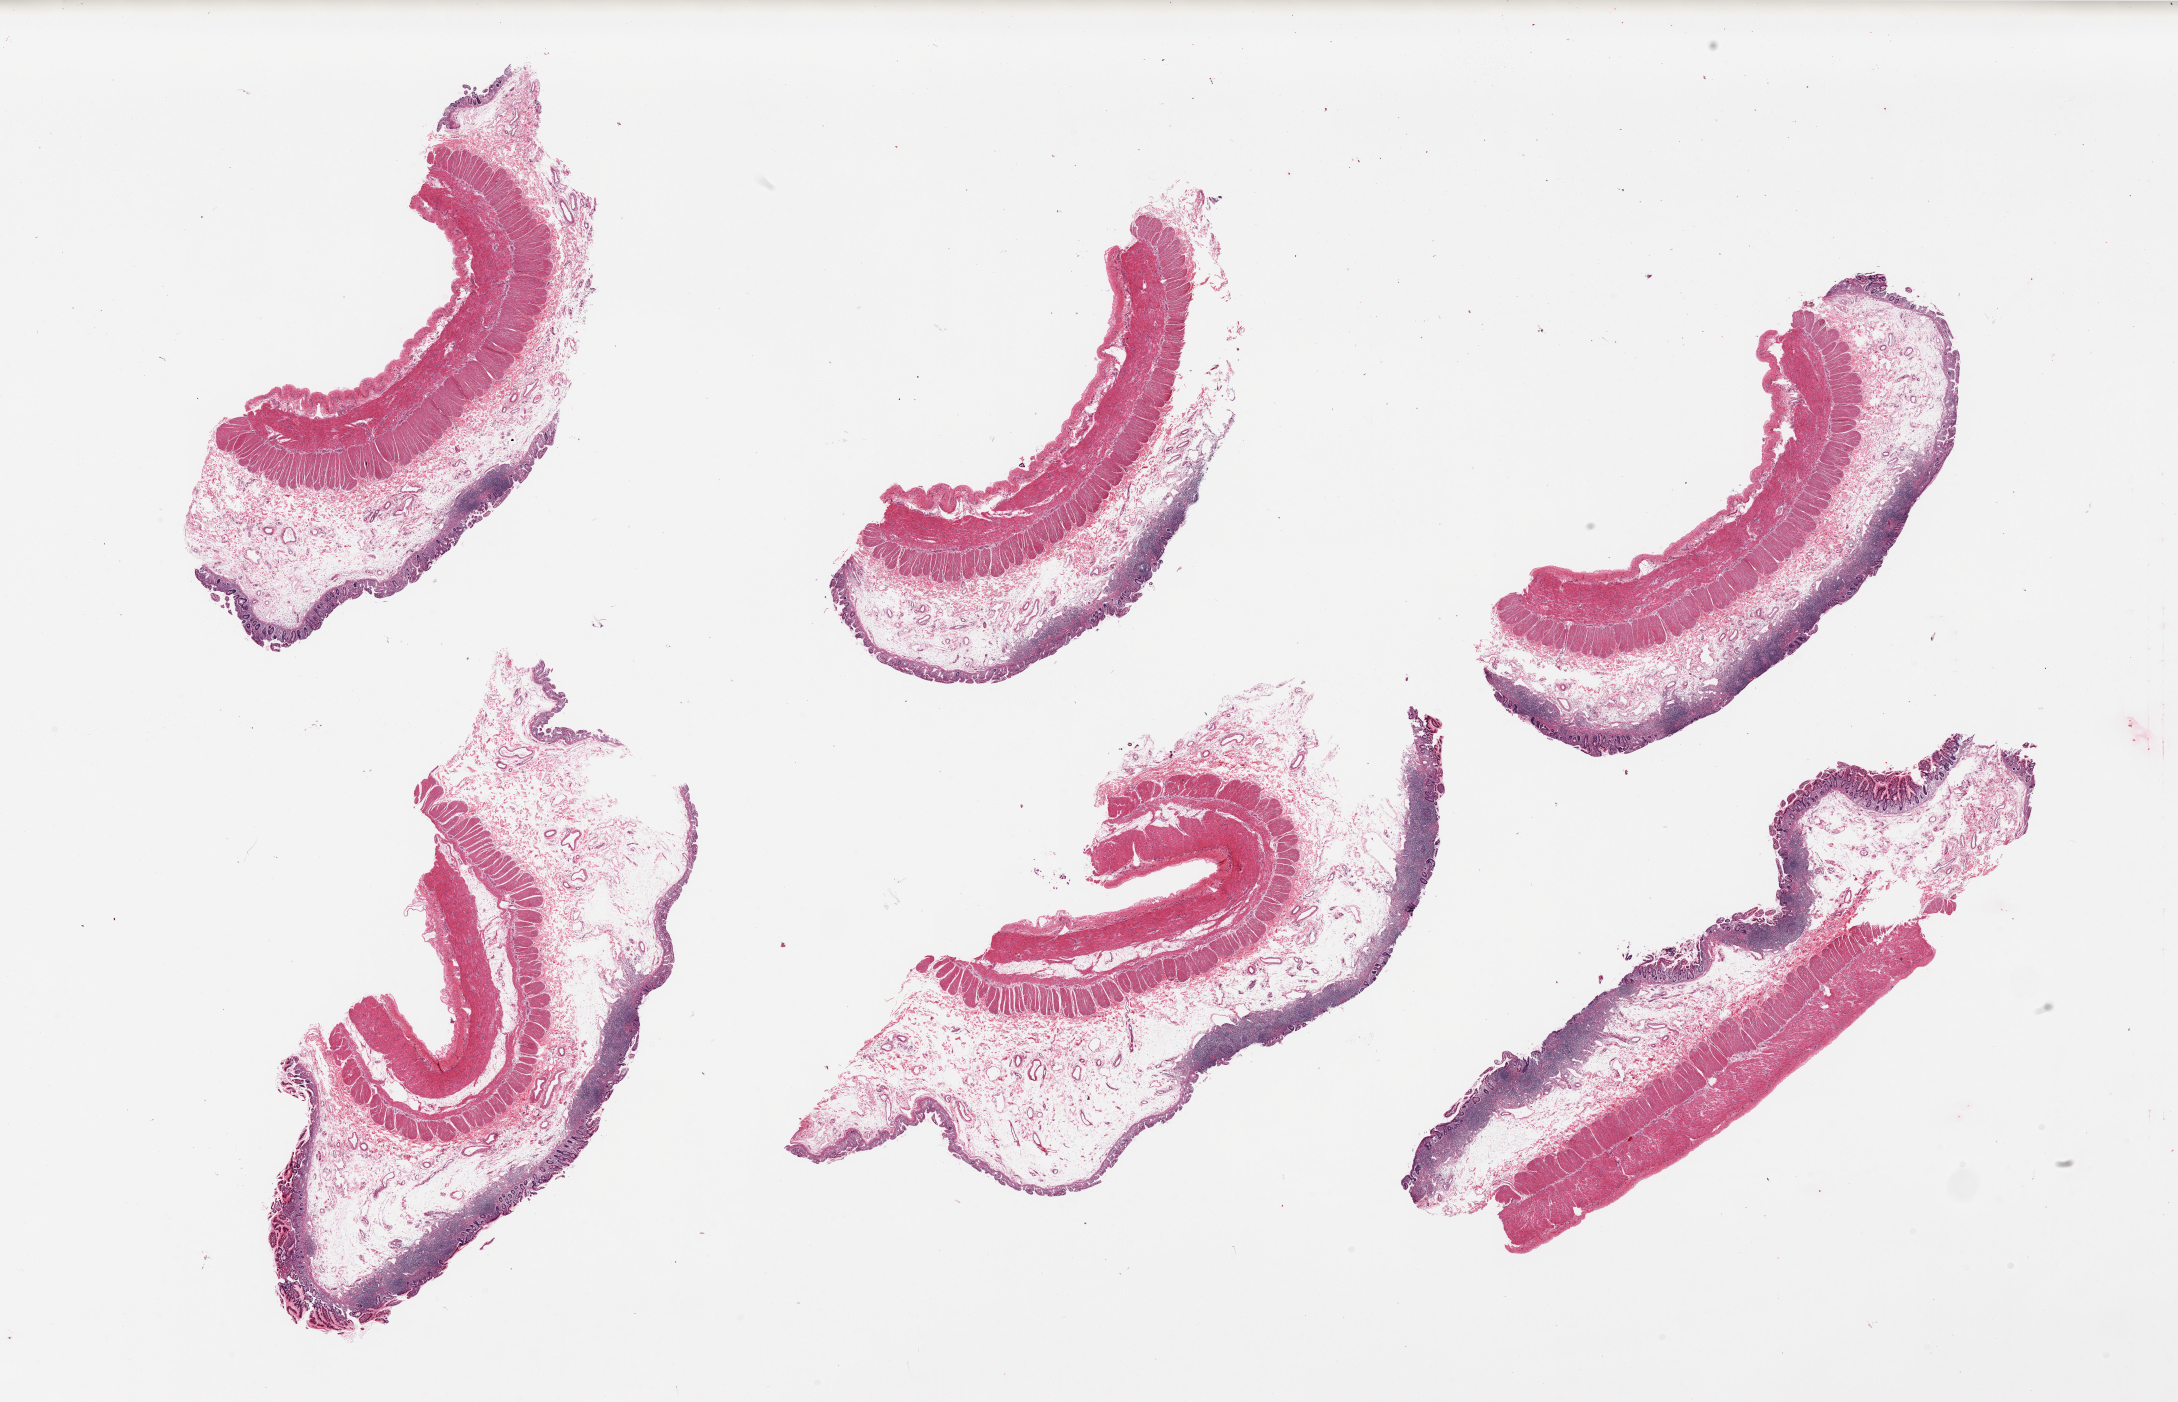
Whole-slide image, haematoxylin and eosin stain, brightfield — low-resolution overview of the scanned area, about 34.5 x 22.2 mm. PAXgene-fixed paraffin-embedded (PFPE) section. Target tissue: ileum. Donor tissue sample. Female donor.
Pathologist's review note for this sample: 6 pieces, clusters of lymphoid tissue, muscularis propria present in all 6 pieces.